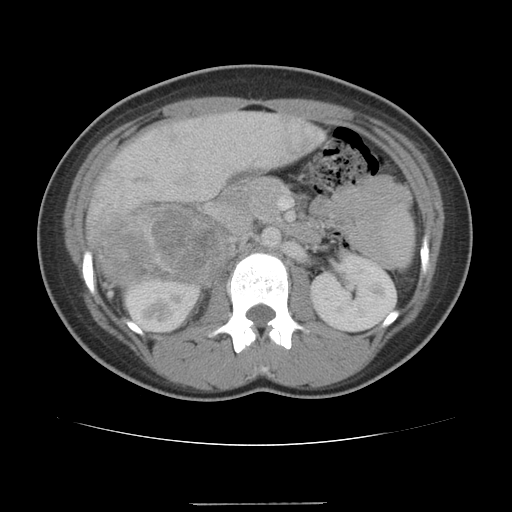
Contrast-enhanced abdominal CT, one axial slice. Slice 63 of 100 in the series (ordered by position). Reconstruction kernel STANDARD. Intravenous contrast given. Soft-tissue window (W 400 / L 40 HU). 512 × 512 image matrix. Female patient, age 21 years. Case-level facts recorded for this patient, not image findings: diagnosis: adrenocortical carcinoma; tumour side: right adrenal; tumour size at pathology: 15.5 cm; Ki-67 index: 26 %; stage (as recorded): 3.
Structures marked on this image (semi-automatically segmented with operator editing):
- mass: box from (x=103, y=207) to (x=227, y=285) px